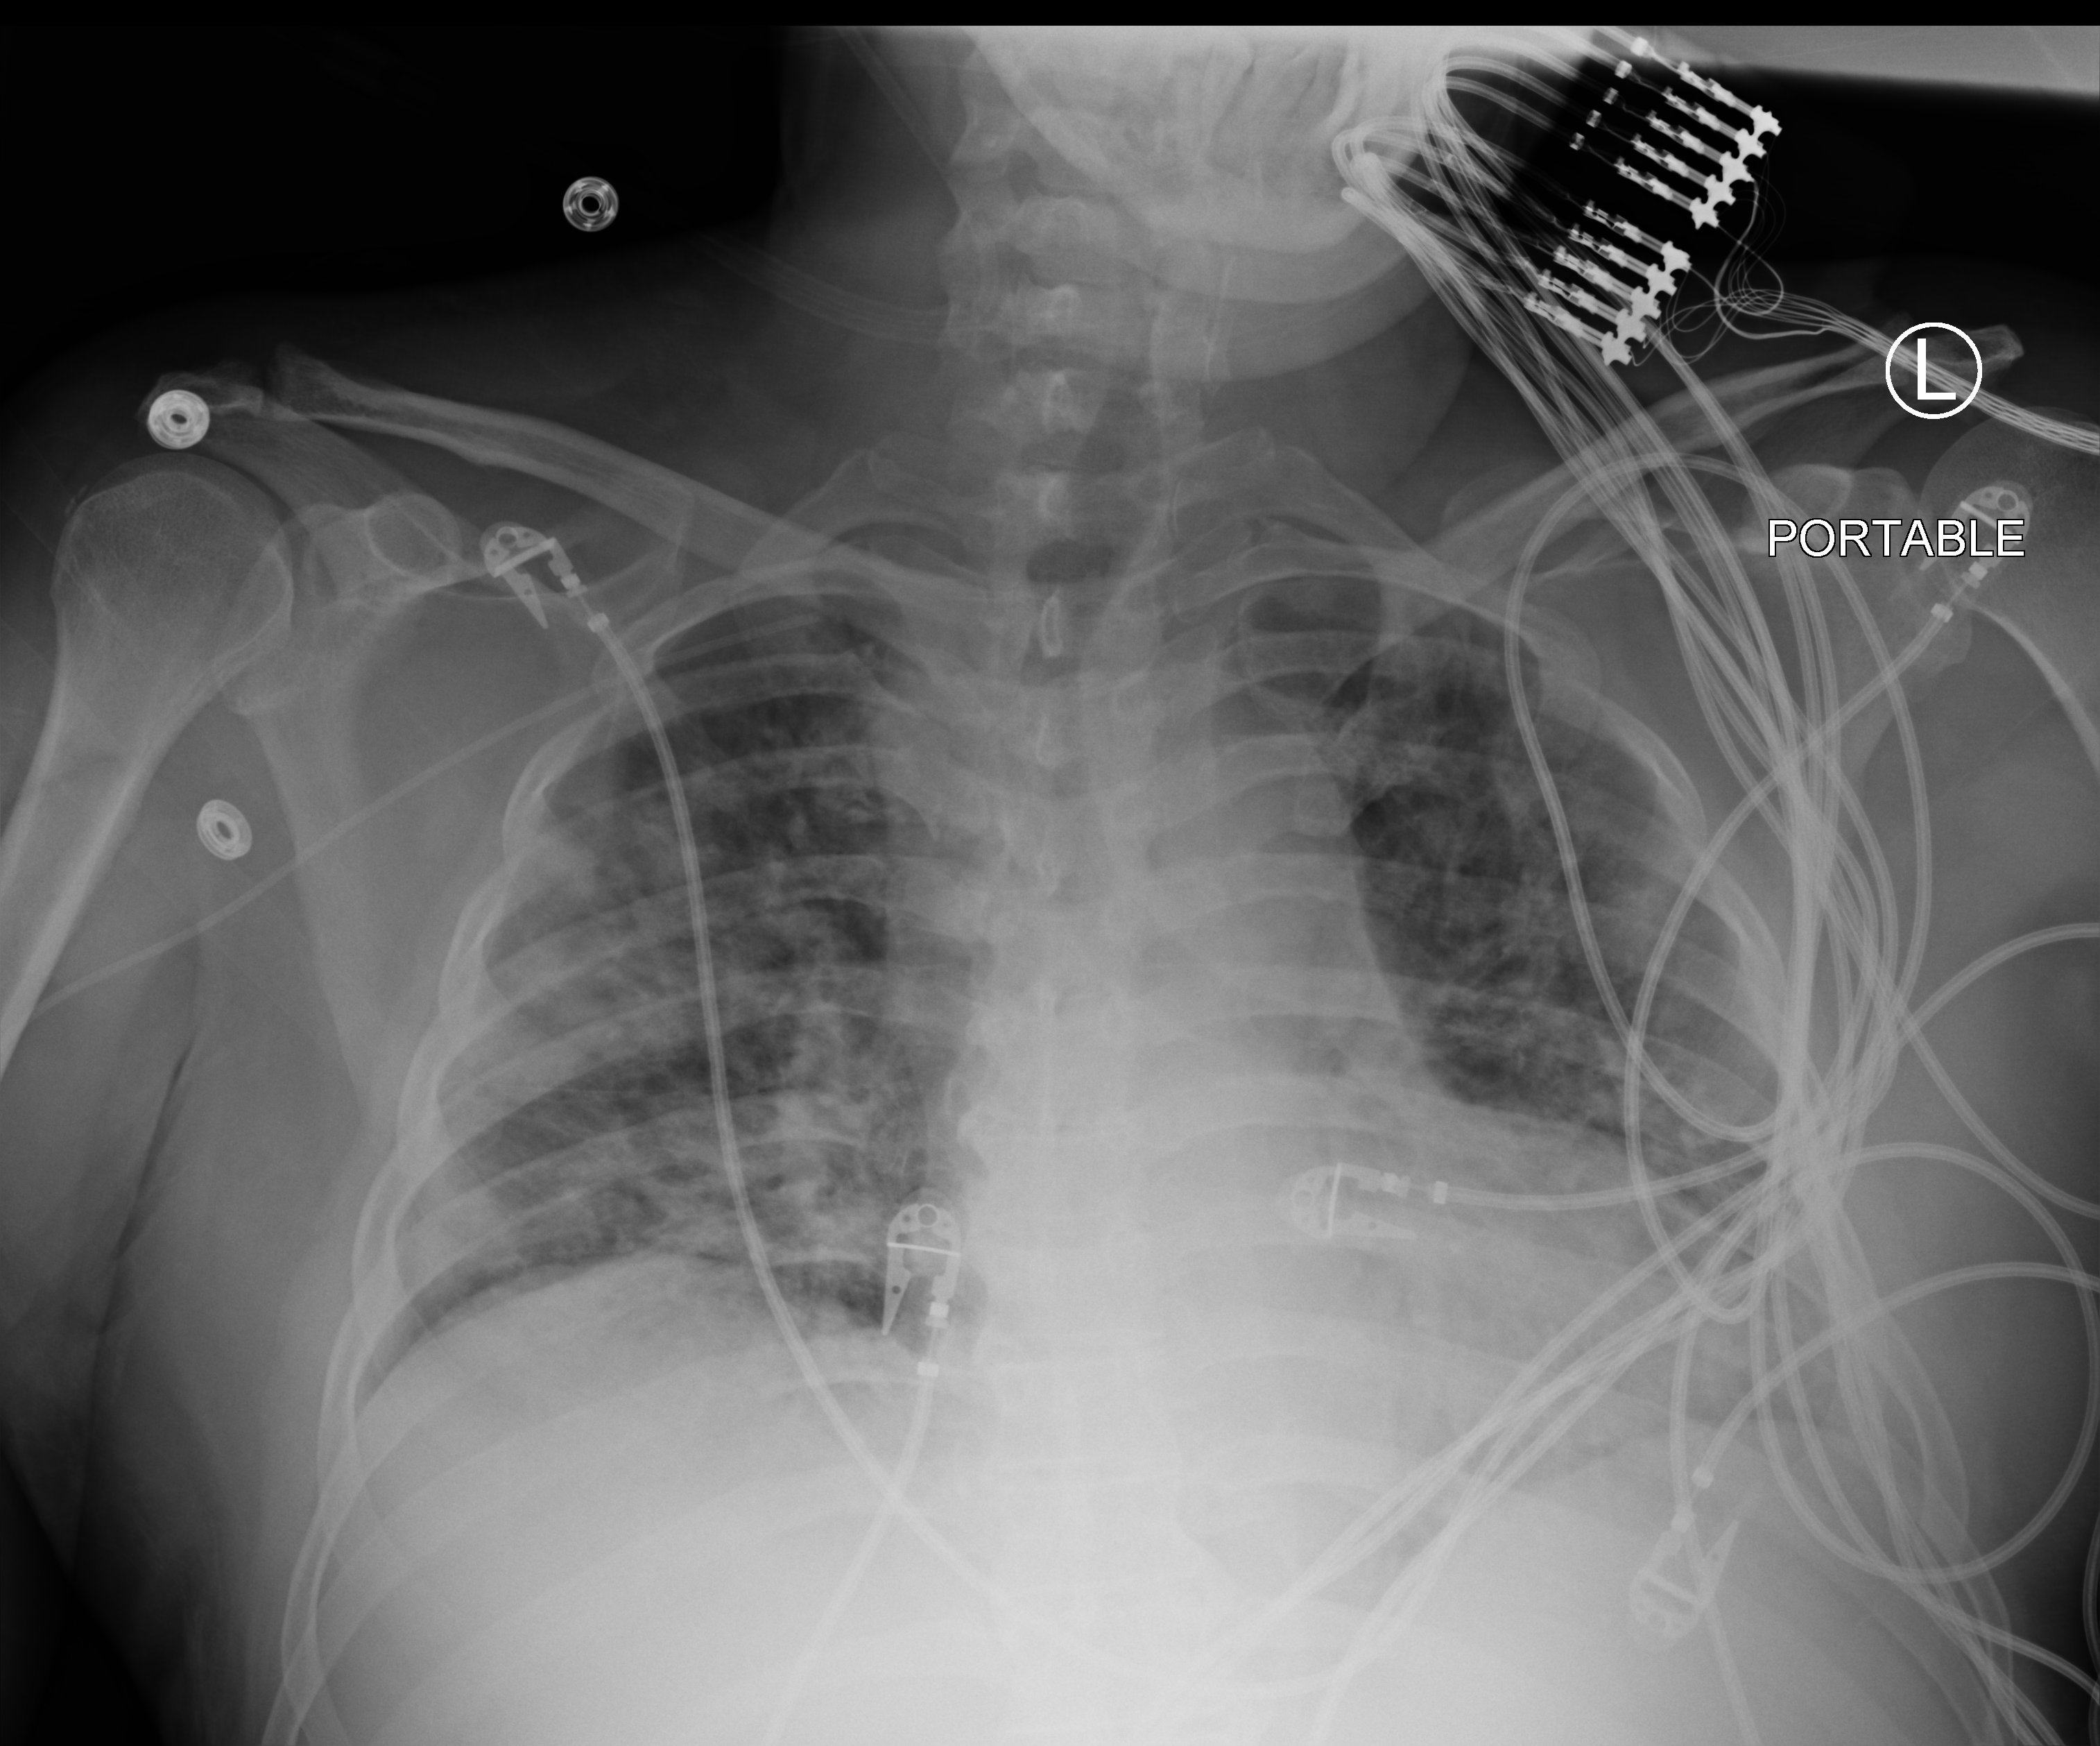
Portable chest radiograph. Male patient hospitalised with COVID-19, age 18–59 years.
Hospital-stay facts (about this admission, not read from this image; timing relative to this image not recorded):
- length of hospital stay: 26 days